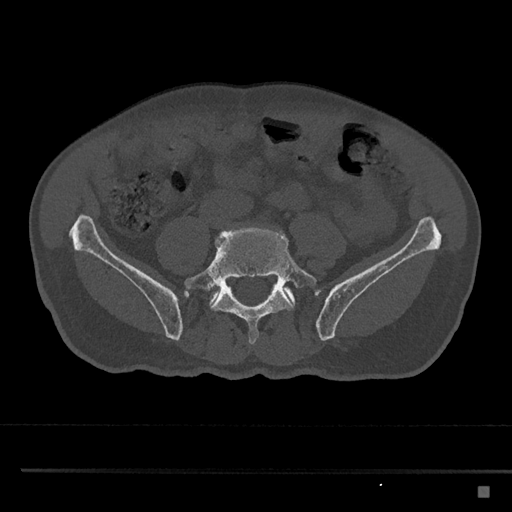
CT including the spine, one axial slice. Slice 579 of 797 in the series (ordered by position). Reconstruction kernel Br40s/3. Bone window (W 1800 / L 400 HU). 512 × 512 image matrix. Male patient, age 59 years. Case-level facts recorded for this patient, not image findings: primary cancer: prostate.
Annotated regions visible in this slice (semi-automatic segmentation, software-assisted and operator-edited):
- L5 vertebra: bounding box [x1, y1, x2, y2] px = [183, 226, 317, 345]